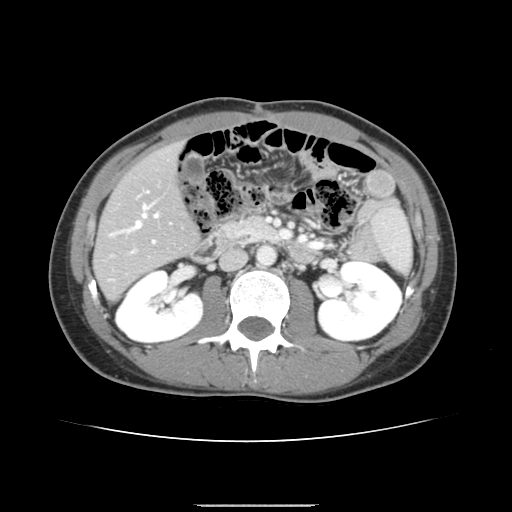
Contrast-enhanced abdominal CT, one axial slice. Position 64 of 150 along the scan axis. 120 kVp. Intravenous contrast given. Soft-tissue window (W 400 / L 40 HU). 2.5 mm slice thickness. 512 × 512 image matrix, field of view 324 × 324 mm. Female patient, age 32 years. Case-level facts recorded for this patient, not image findings: diagnosis: colorectal cancer liver metastases, imaged before liver resection; multiple liver metastases: yes; largest metastasis: 0.7 cm; disease in both lobes: no.
Outlined on this slice (outlined manually by an expert reader):
- hepatic veins: bounding box [x1, y1, x2, y2] px = [127, 204, 158, 231]
- liver: [95, 146, 198, 299]
- planned liver remnant (the part of the liver to remain after resection): [95, 147, 198, 293]
- portal vein (with intrahepatic branches): [110, 190, 155, 252]